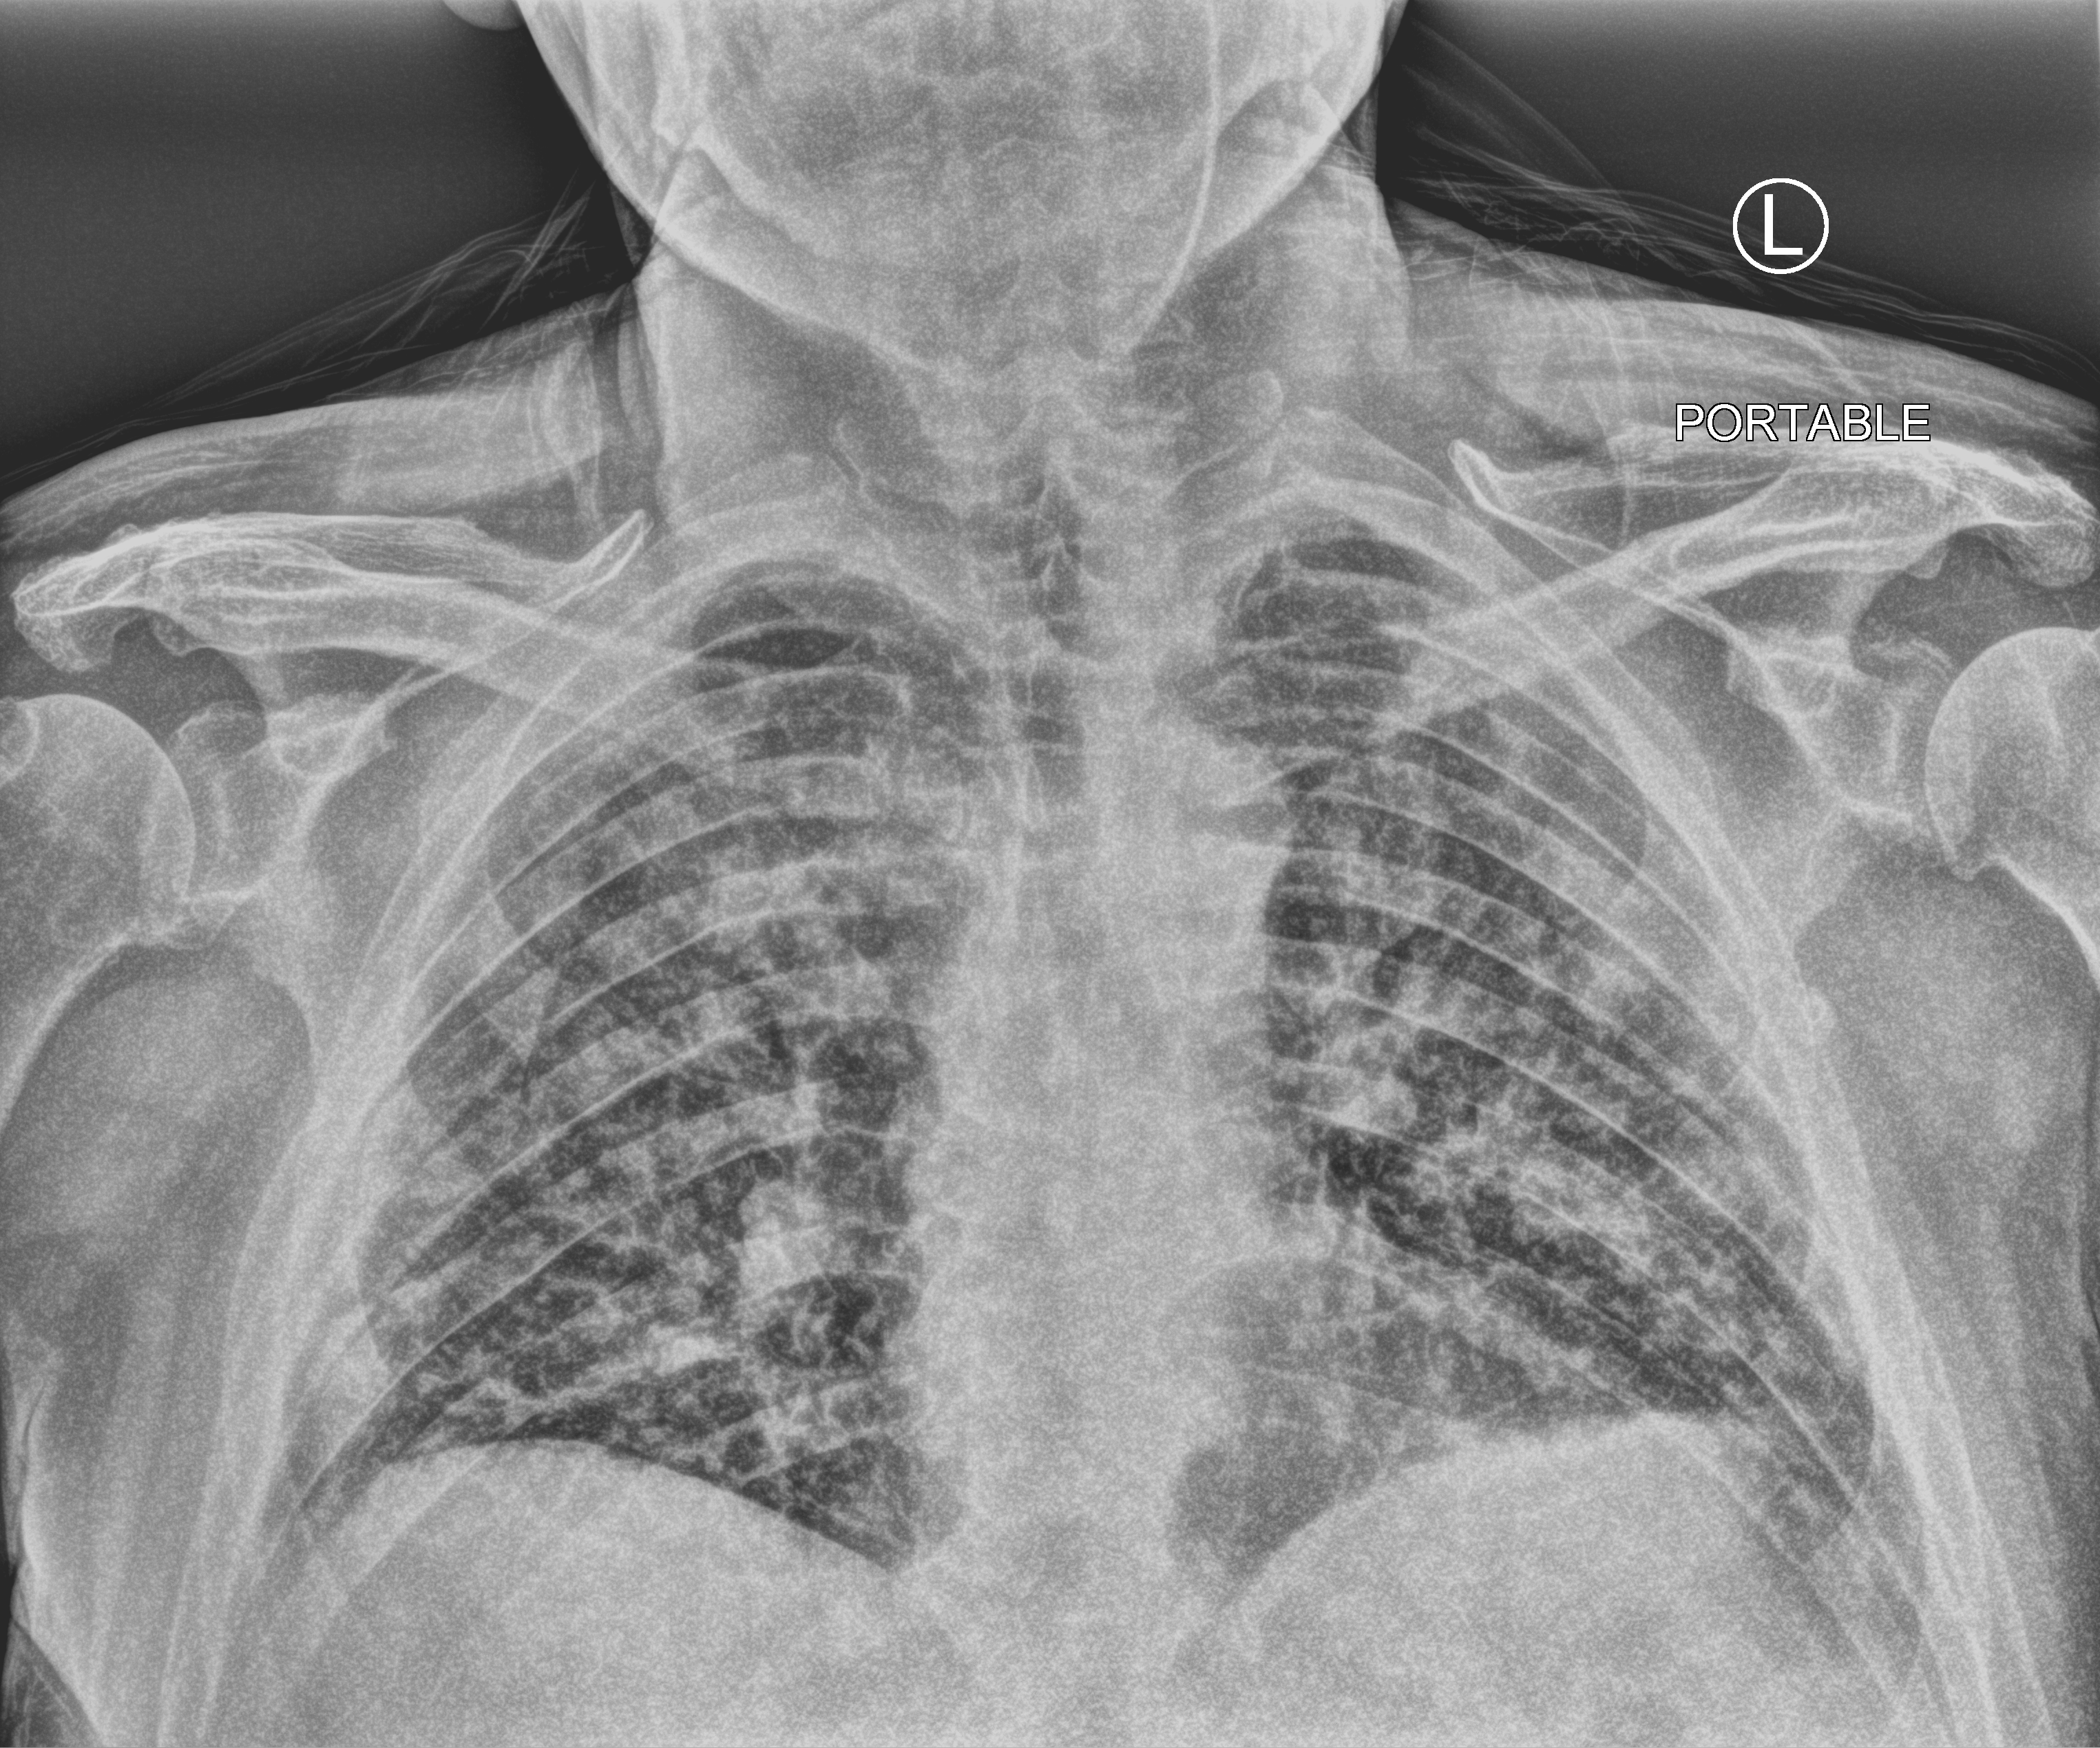
Bedside chest radiograph (computed radiography); anteroposterior (AP) projection. Male patient hospitalised with COVID-19, age 60–74 years.
Admission-level facts for this patient (not findings on this image; timing relative to this image not recorded):
- admitted to intensive care during this hospital stay: no